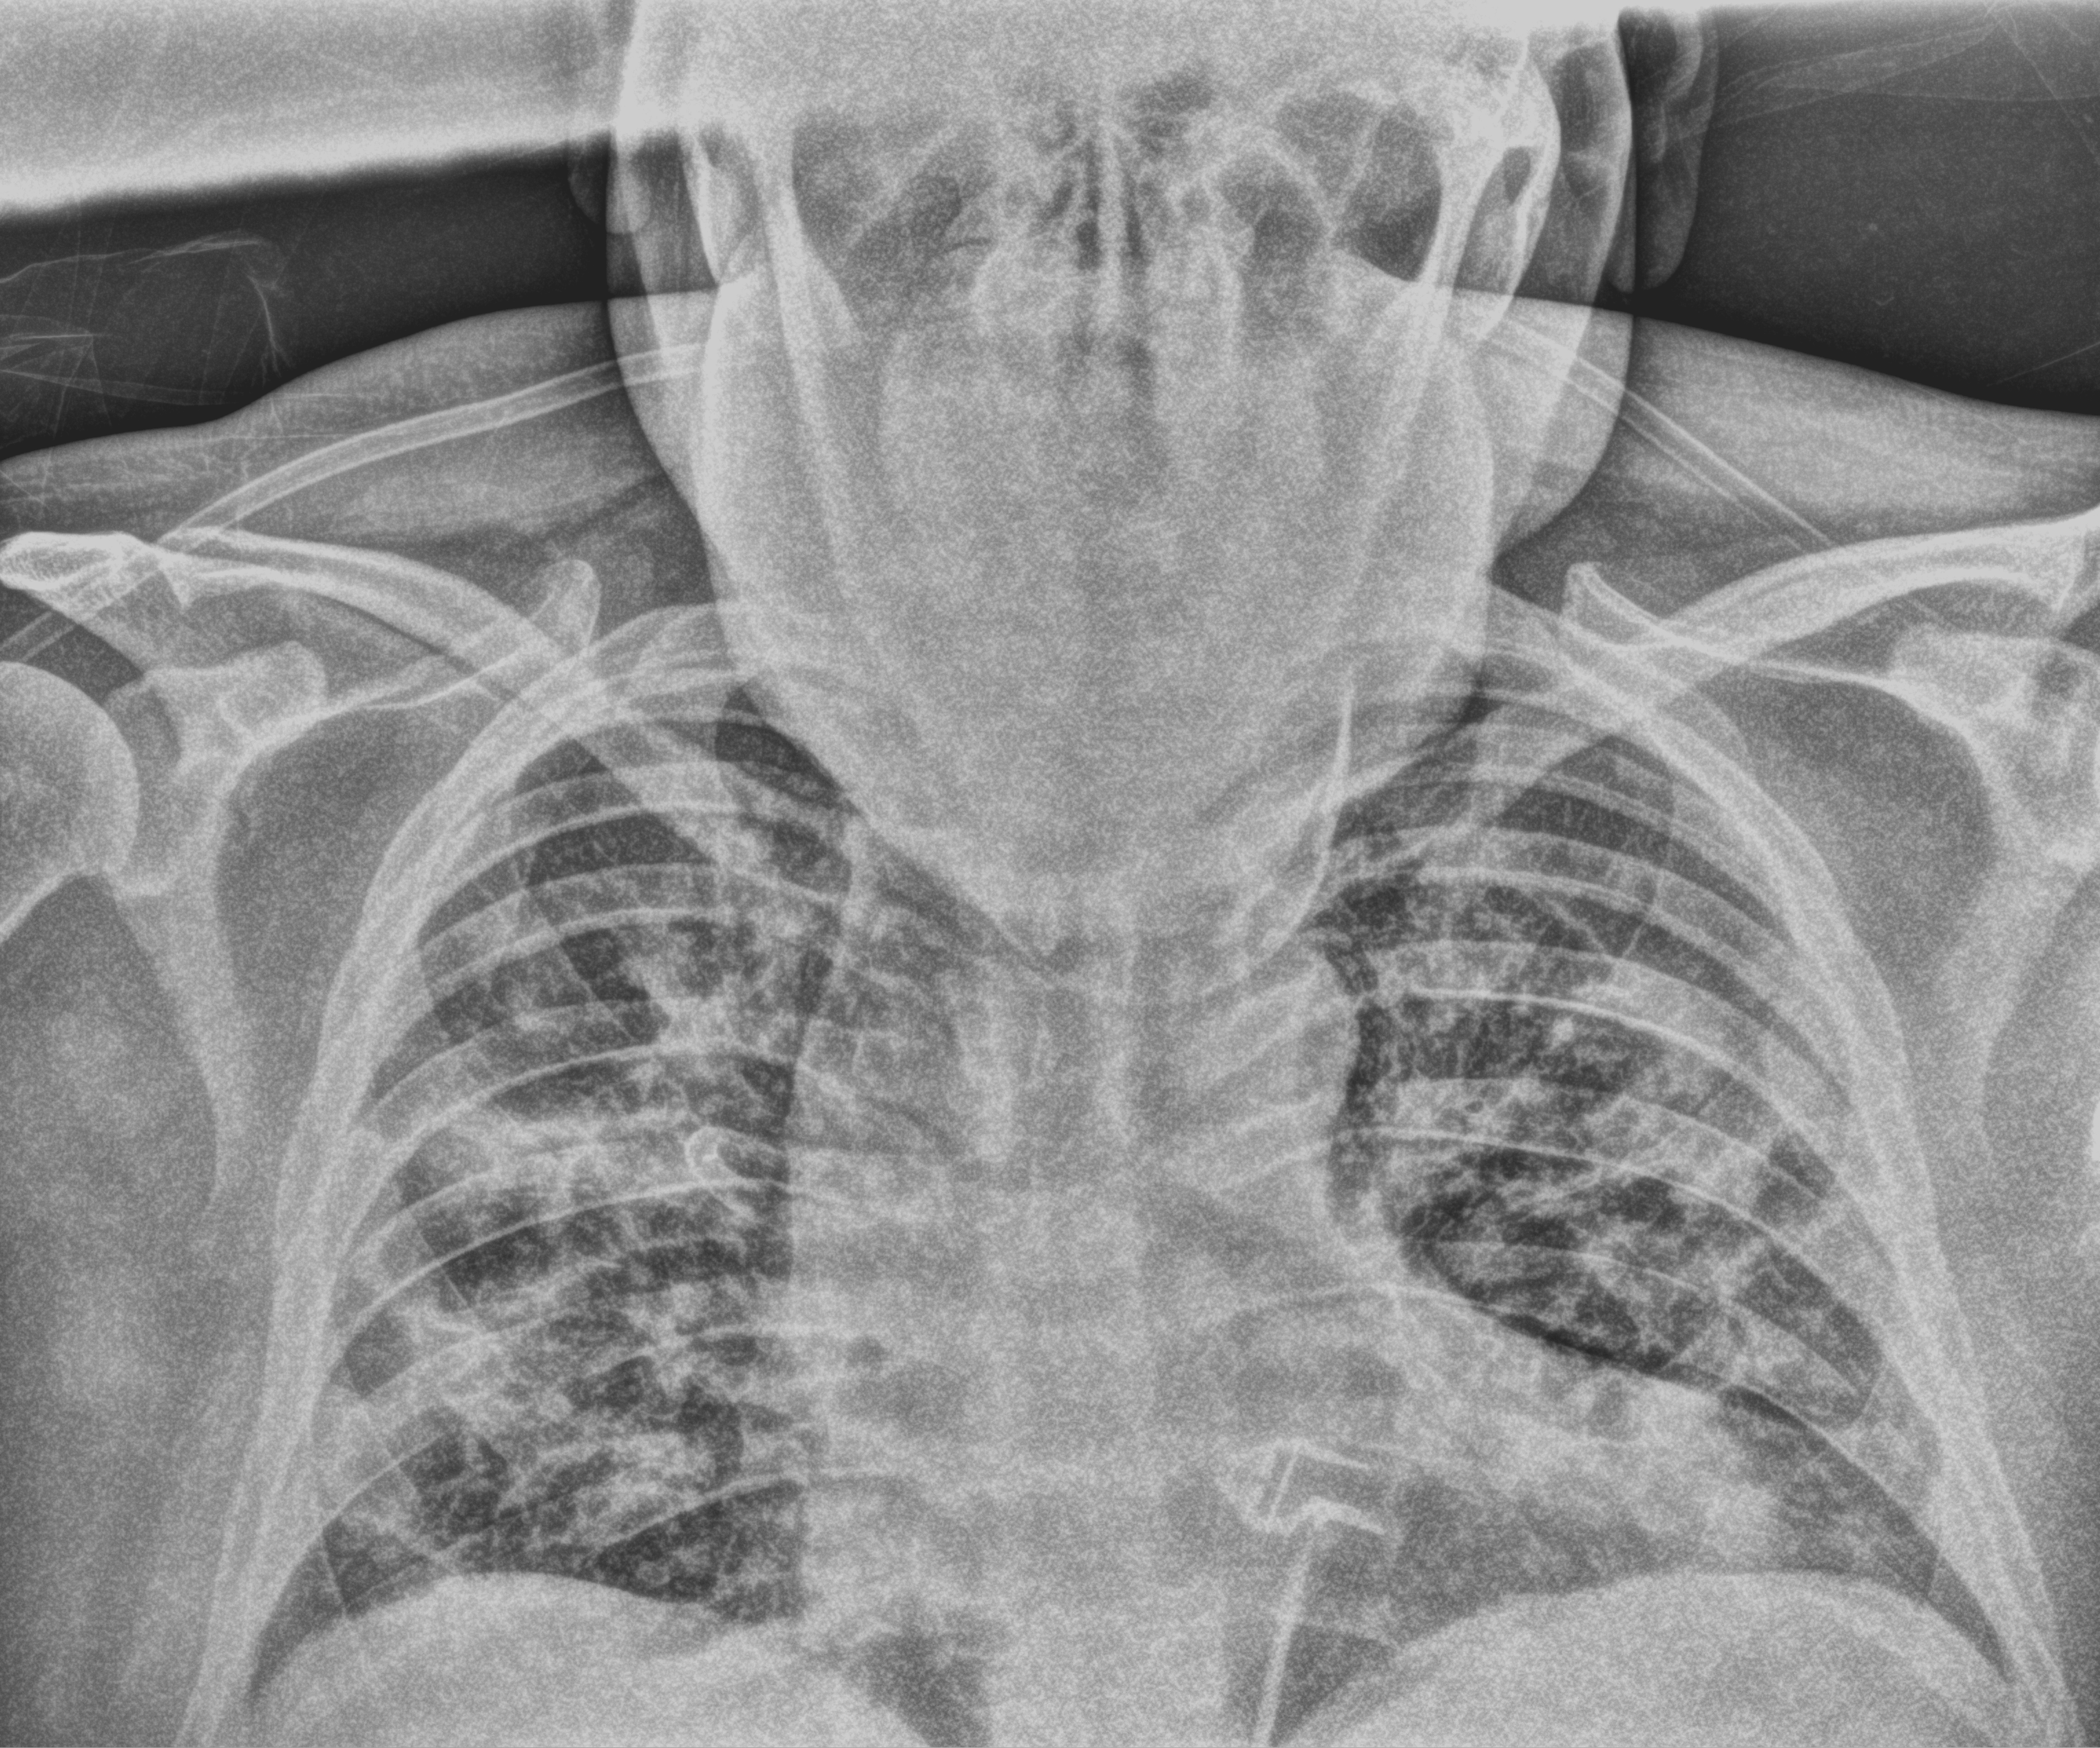
Bedside chest radiograph (computed radiography), anteroposterior (AP) projection. Male patient hospitalised with COVID-19, age 18–59 years.
From the hospital-stay record, not from the radiograph (when in the stay this image was taken is not recorded):
- length of hospital stay: 20 days
- mechanically ventilated during this hospital stay: no
- admitted to intensive care during this hospital stay: no